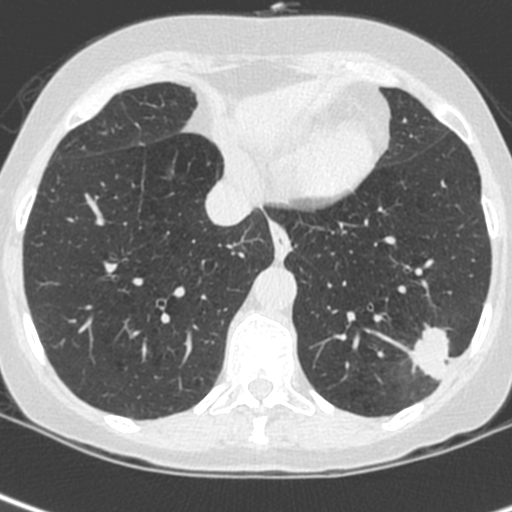
Low-dose screening chest CT, axial slice, baseline annual screen, lung window (W 1500 / L -600 HU), 1.3 mm slice thickness, 120 kVp. Female participant, aged 56 years at enrolment.
Expert-annotated lung lesion, box from (x=407, y=322) to (x=474, y=389) px. Screening reader's record for this exam (one nodule recorded; not confirmed to be the boxed lesion): non-calcified nodule or mass ≥4 mm, left lower lobe, 37 × 29 mm, spiculated (stellate) margins, ground glass attenuation. Lung cancer was diagnosed 91 days after this screen: squamous cell carcinoma, NOS, left lower lobe, poorly differentiated (G3), stage IIIA (AJCC 6th edition), 35 mm at pathology.